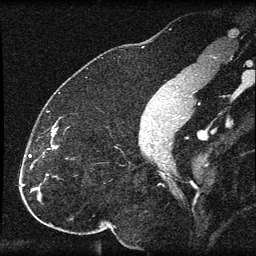
Breast MRI (dynamic contrast-enhanced), one sagittal slice; position 34 of 60 along the scan axis; dynamic contrast-enhanced series, image 2 of 3 at this slice position (ordered by acquisition); 1.5 T; TE 4.2 ms, TR 8.2 ms; 2 mm slice thickness; 256 × 256 image matrix, field of view 180 × 180 mm. Female patient, age 32 years.
Outlined on this slice (semi-automatic segmentation, software-assisted and operator-edited):
- analysis volume of interest (the breast-tissue region the enhancement analysis was run in; not a lesion): bounding box <31,131,58,184> (left, top, right, bottom; pixels)
- tumour enhancement mask (voxels above the 70 % enhancement threshold inside the analysis volume of interest): <52,132,56,149>